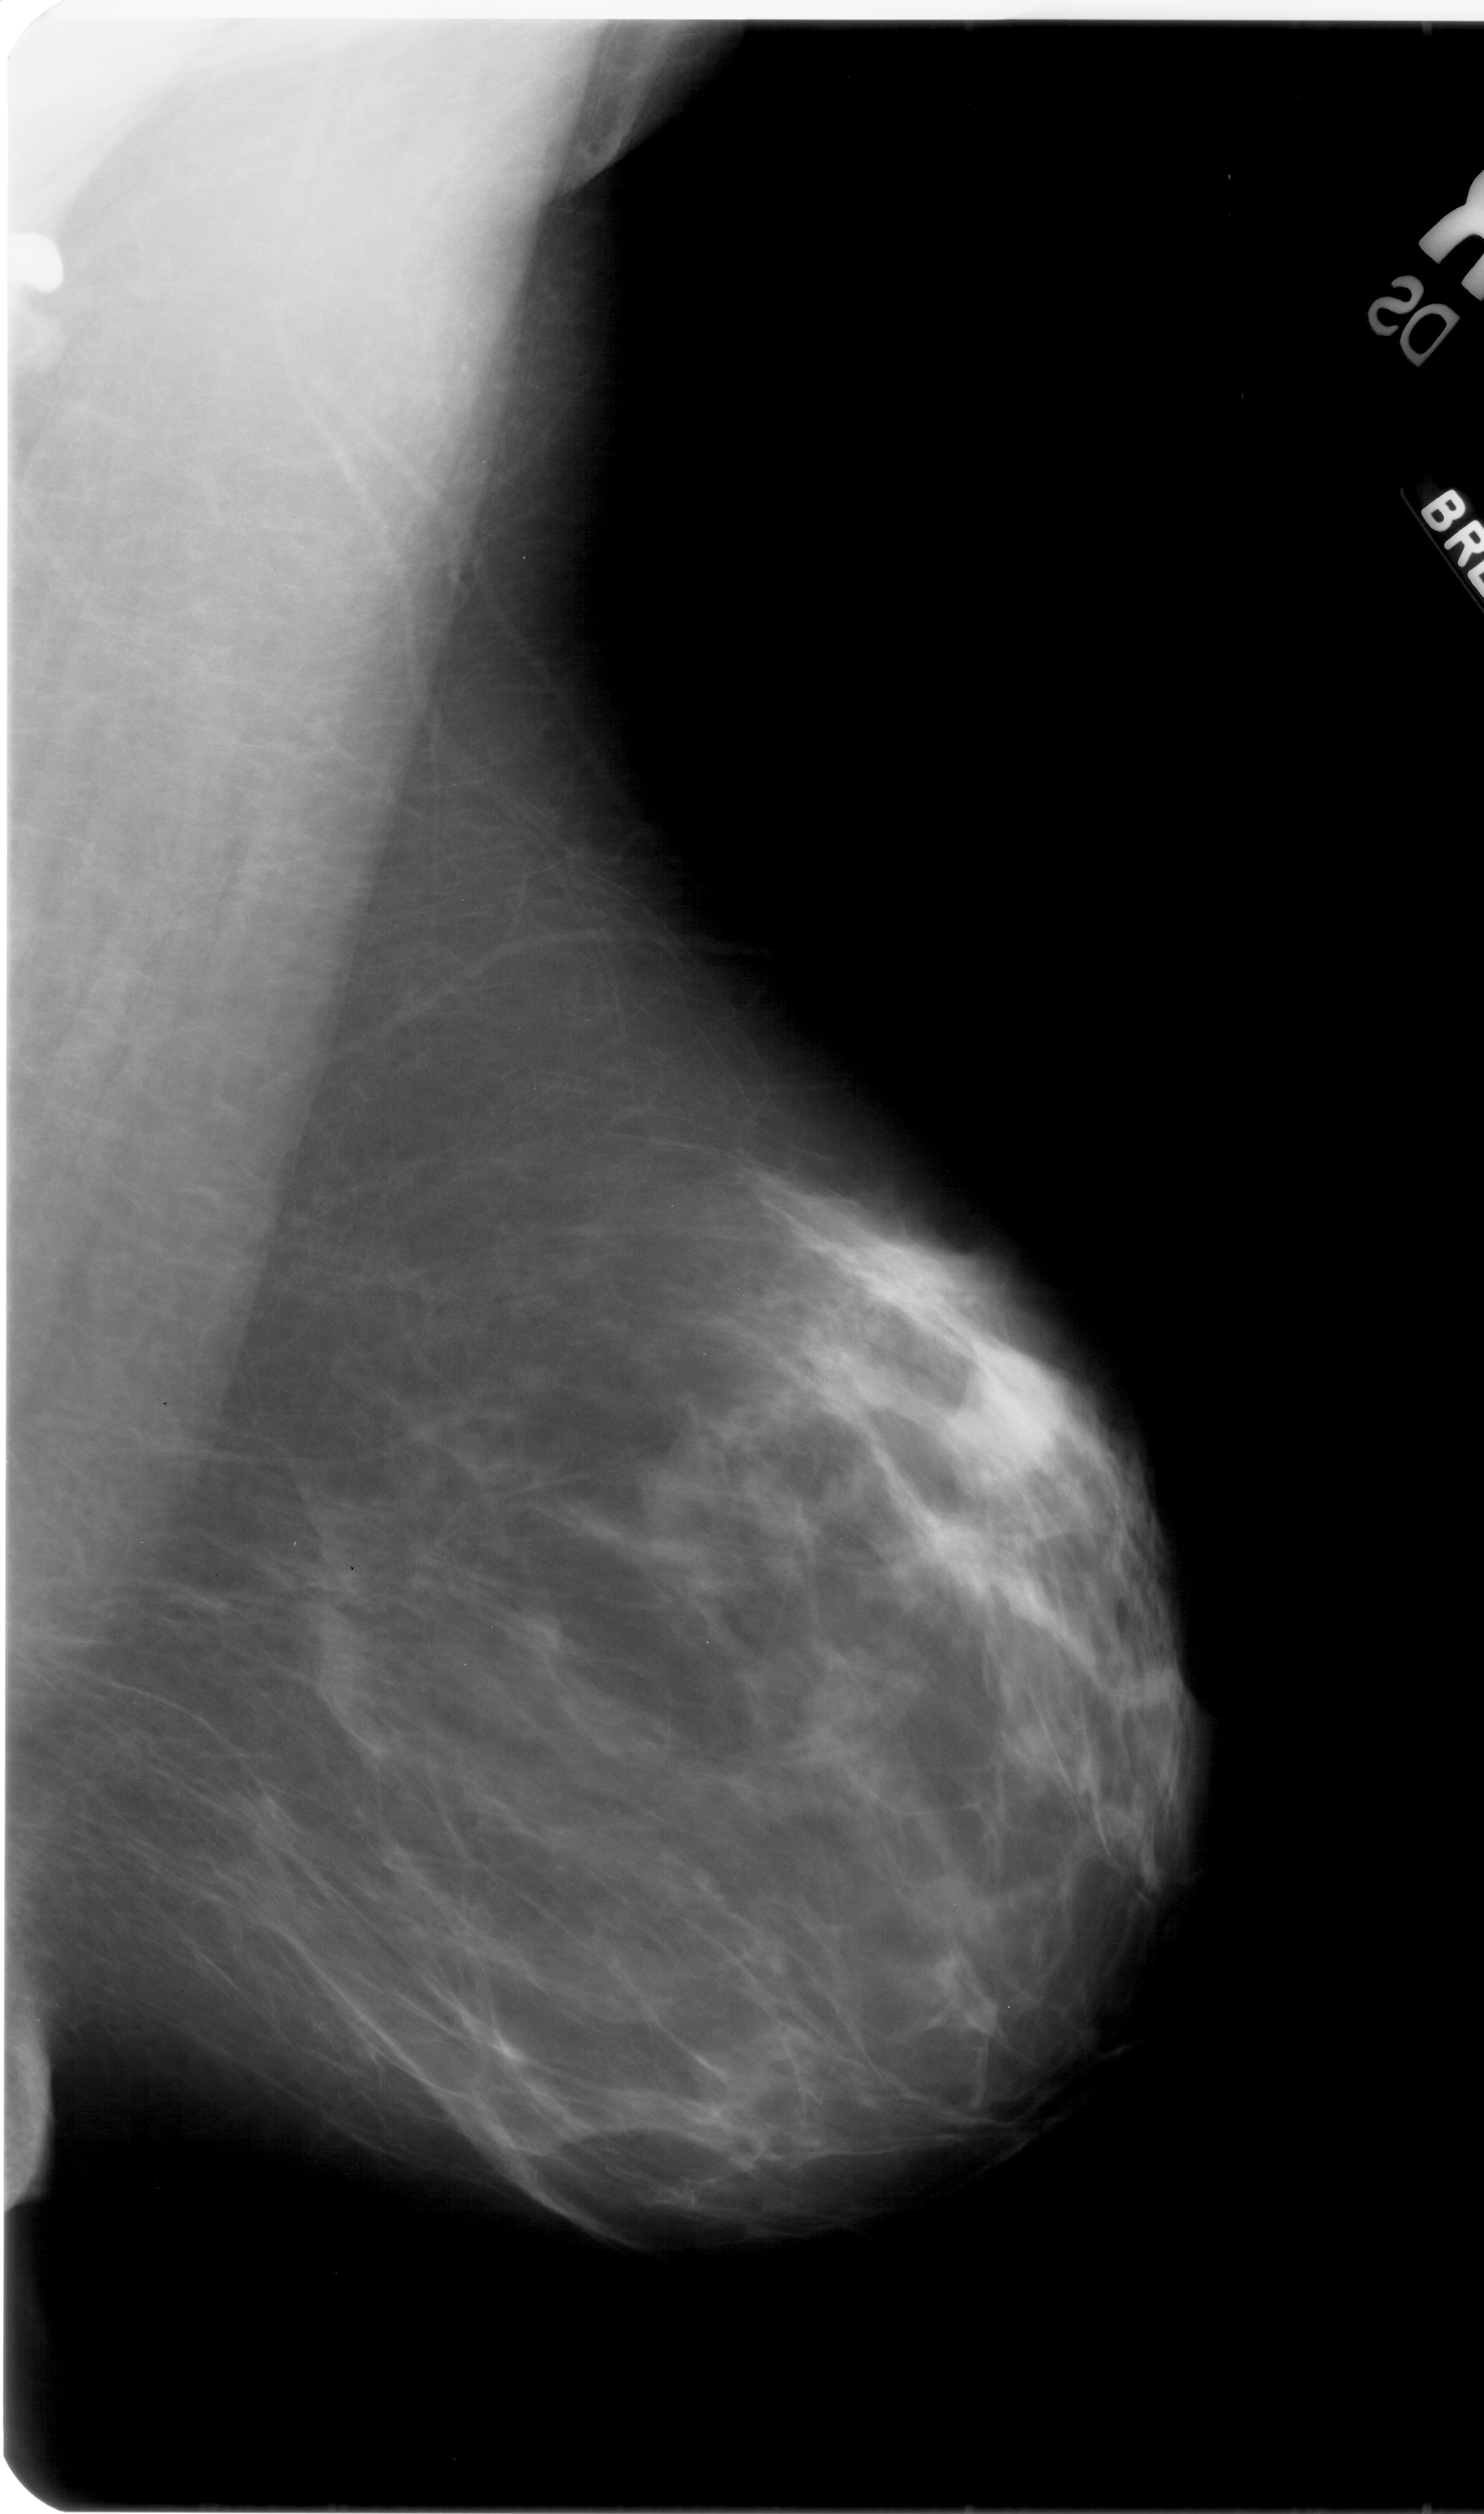
Mammogram (digitized film), right breast, mediolateral oblique (MLO) view, BI-RADS breast density category 2 (scale 1–4).
Radiologist-marked abnormalities on this image: mass, shape lobulated, margins ill defined; BI-RADS assessment category 4; pathology result (as recorded, not read from the image): benign.